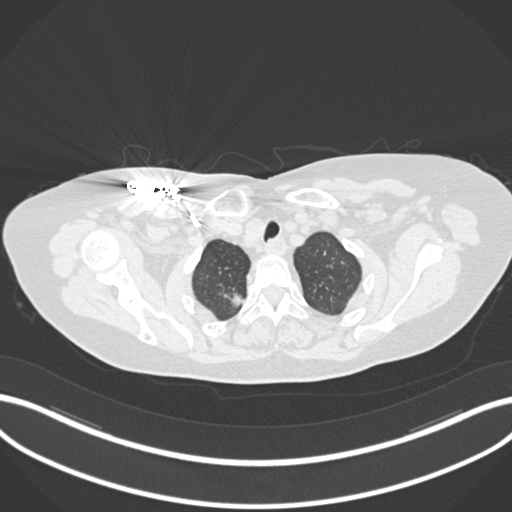
Chest CT, one axial slice. Position 161 of 176 along the scan axis. Reconstruction kernel B30f. Lung window (W 1500 / L -600 HU). 1 mm slice thickness. 512 × 512 image matrix, field of view 400 × 400 mm. Female patient, age 72 years. Case-level facts recorded for this patient, not image findings: clinical TNM (as recorded): T1c N0 M0.
Outlined on this slice (rectangle marked by the reading radiologist):
- lung tumour (recorded histology: adenocarcinoma): bounding box <219,287,244,310> (left, top, right, bottom; pixels)